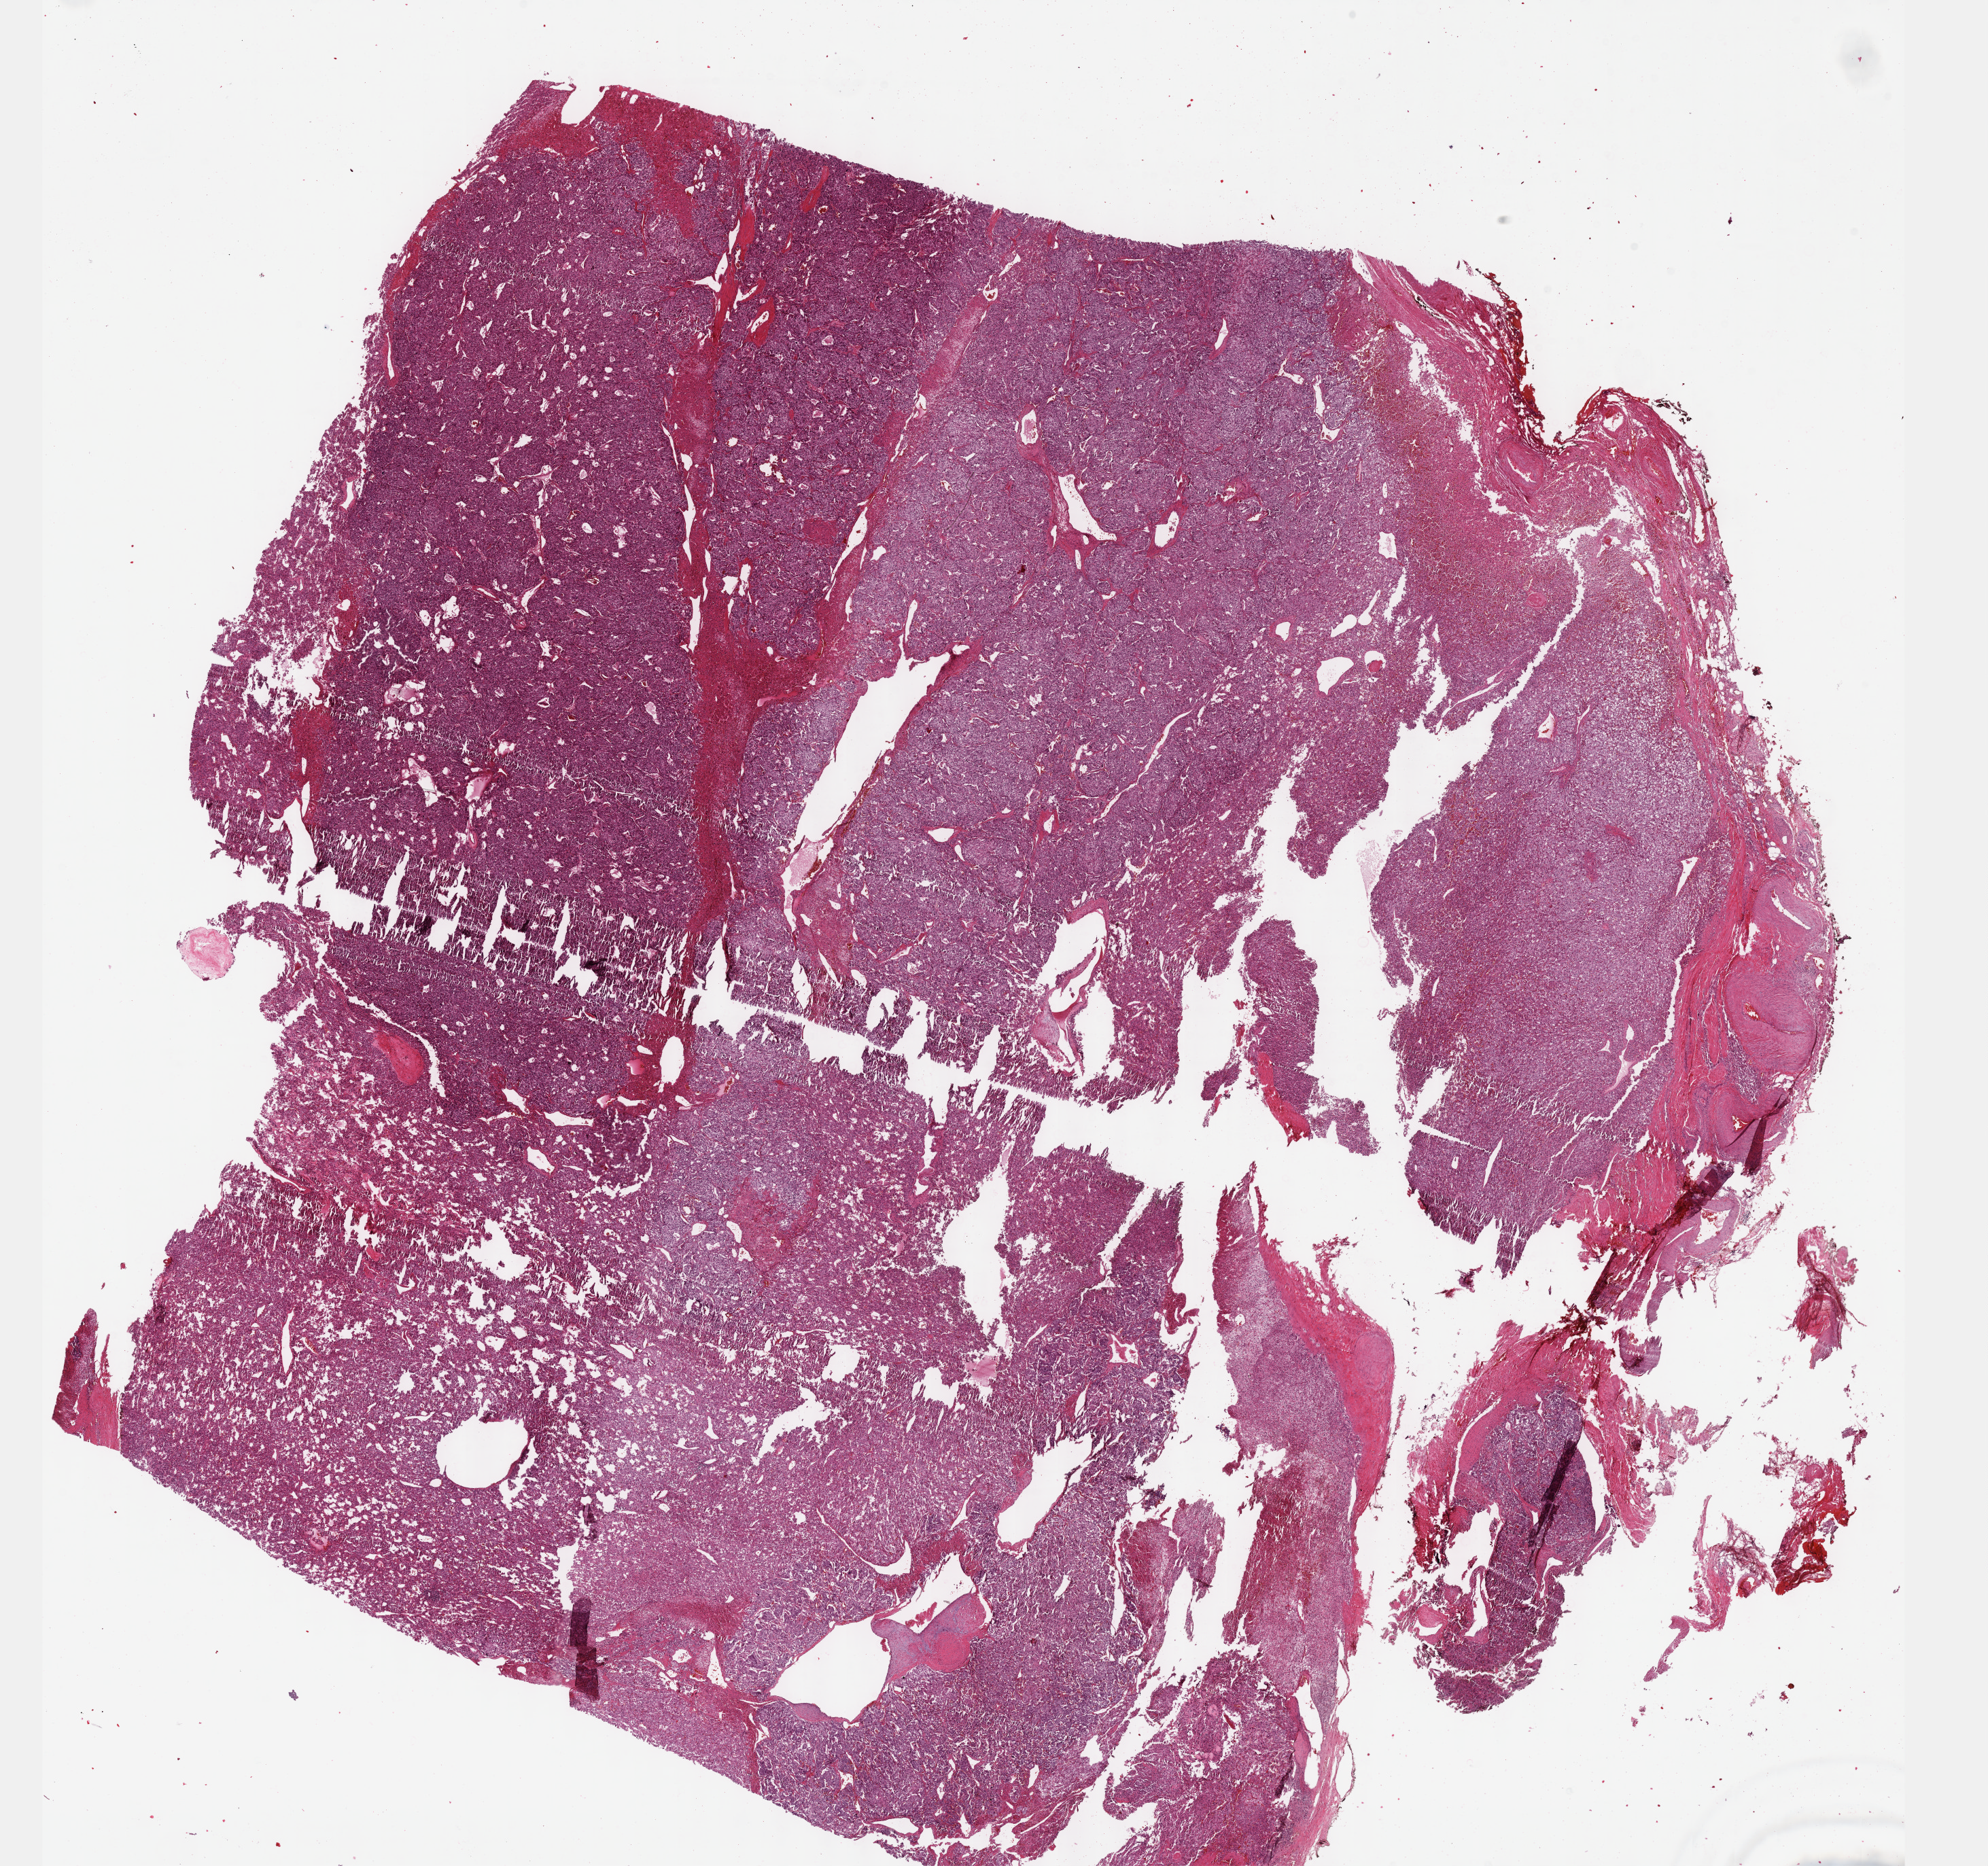
Digitized H&E-stained tissue section (whole slide) — shown as a low-resolution overview of the whole scanned area (about 23.6 x 22.2 mm, acquisition: 40x scan). FFPE section. Sample: primary tumour, adrenal gland. Male, age 49 years at initial diagnosis.
Laterality: right. Diagnosis: Pheochromocytoma, NOS.